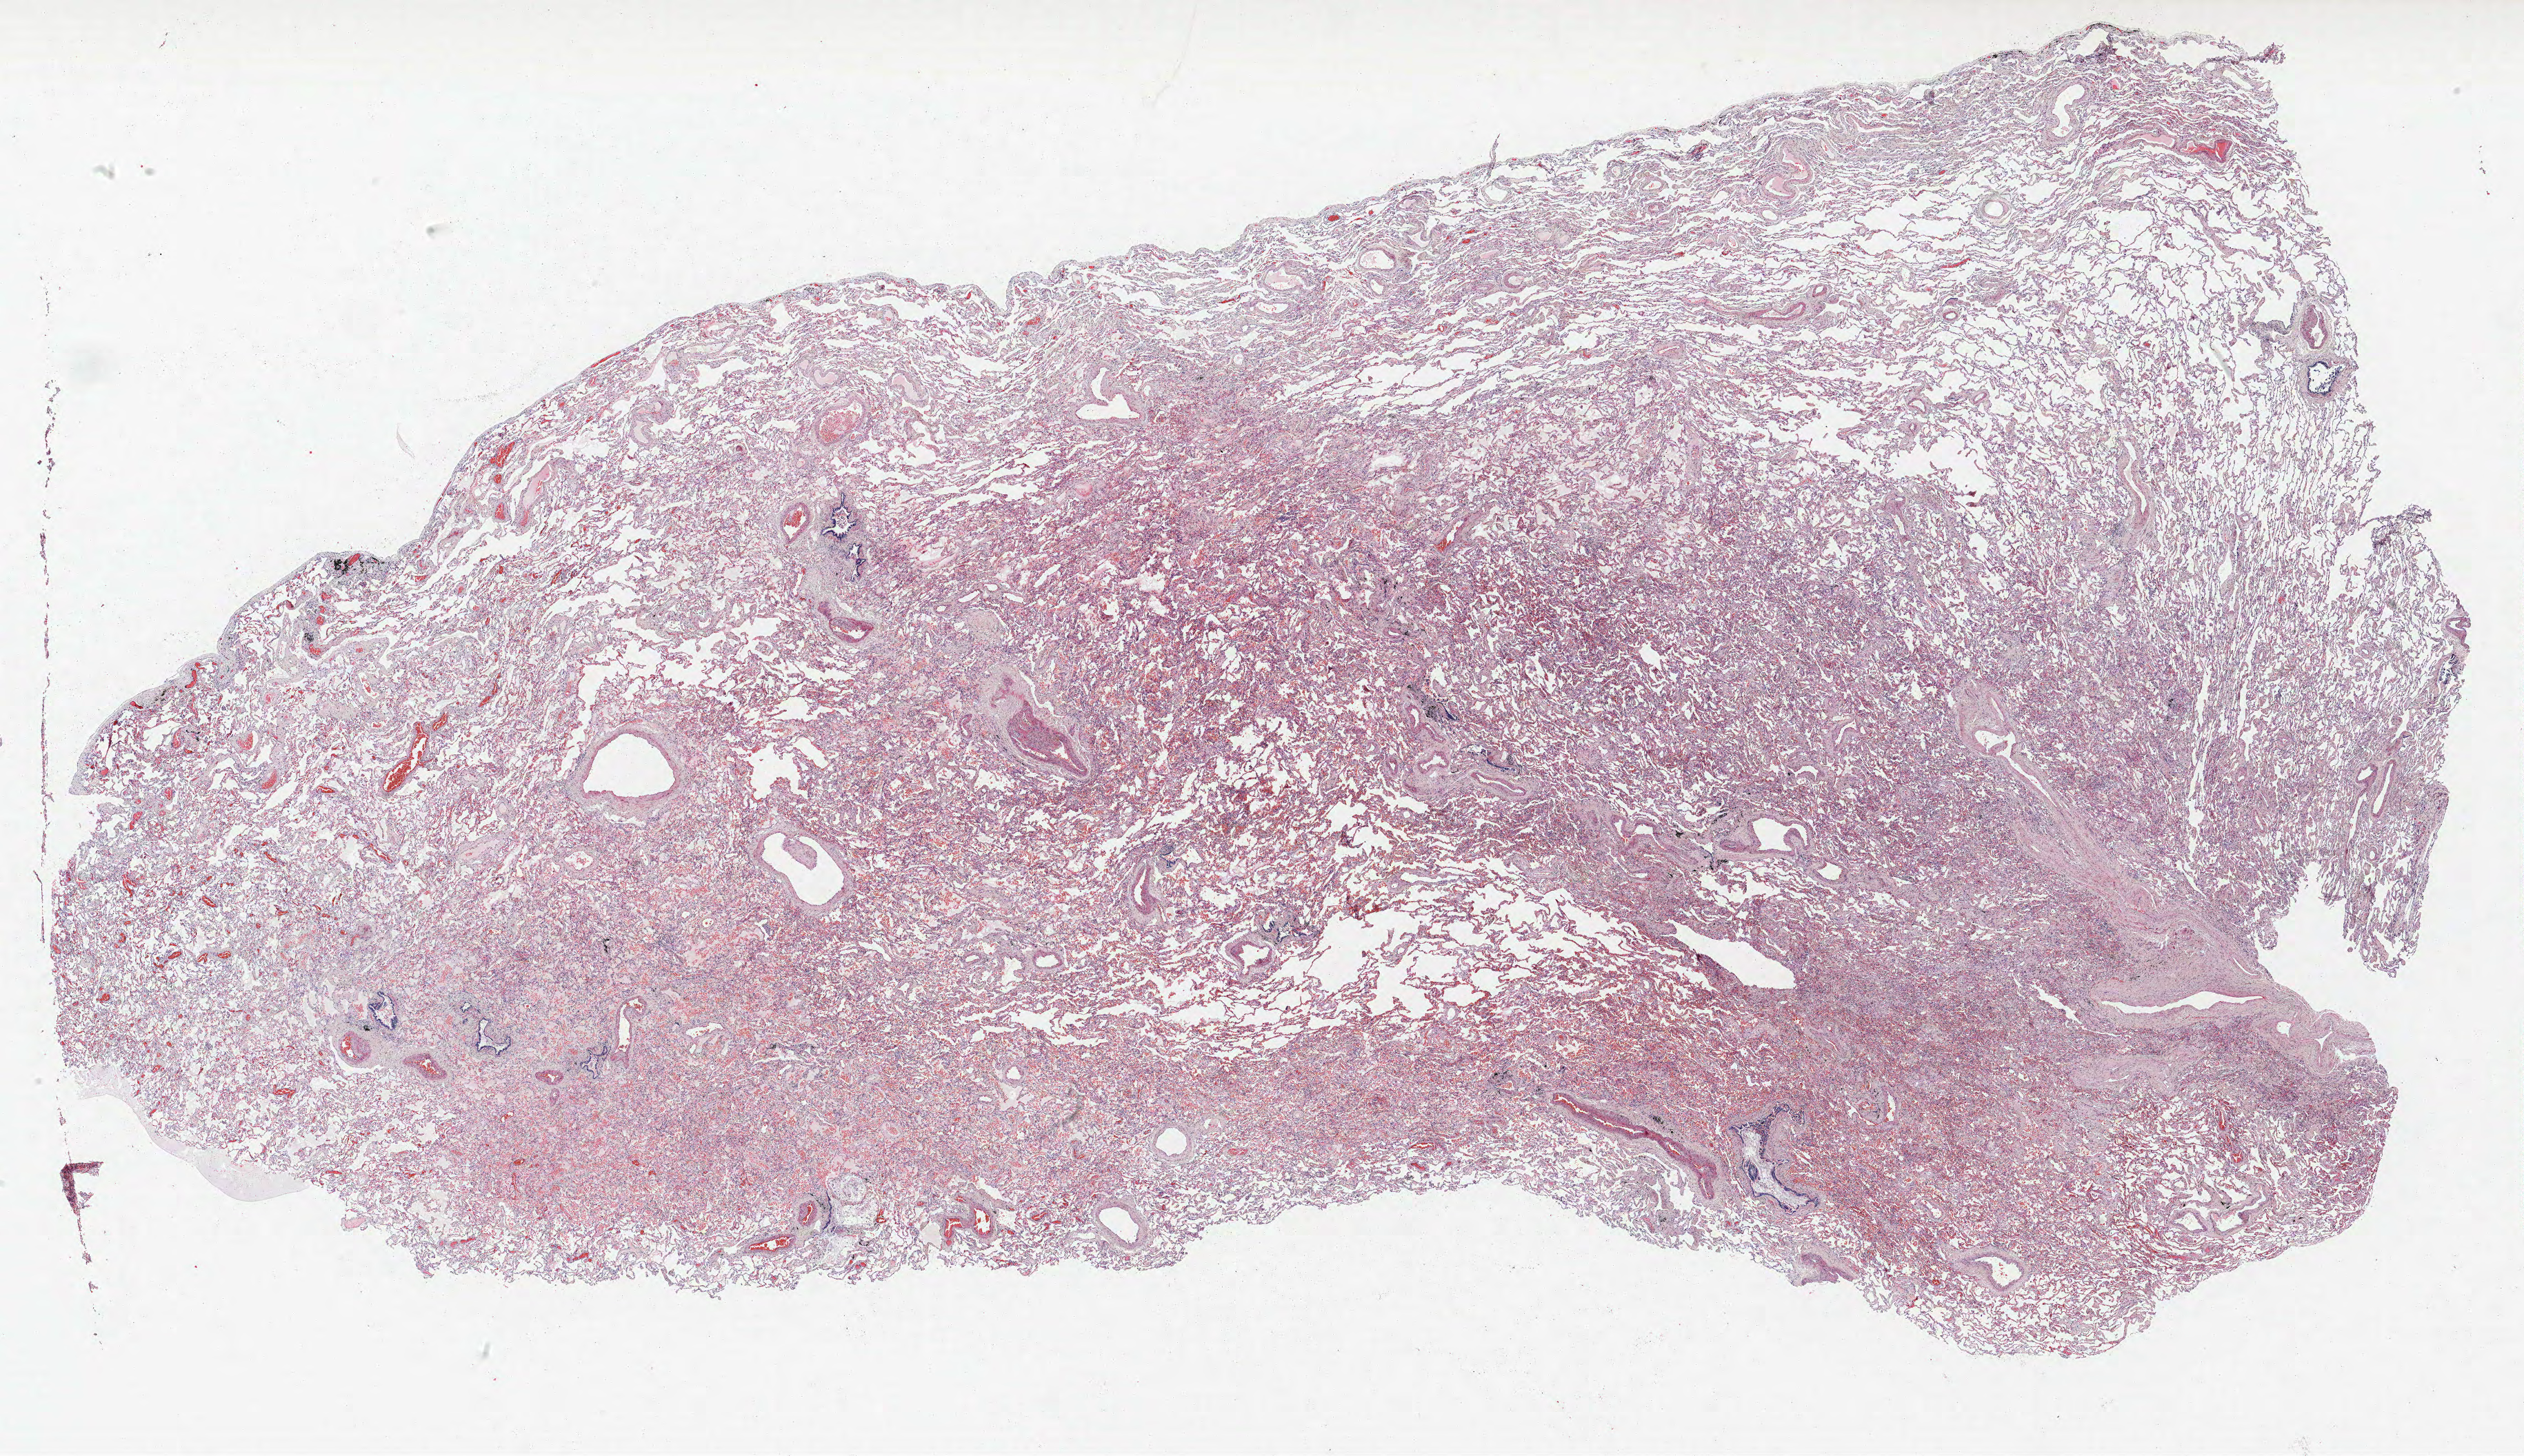
H&E whole-slide image — low-resolution overview of the scanned area, about 29.3 x 16.9 mm (acquisition: 40x scan), formalin-fixed paraffin-embedded (FFPE) section, lung. Female, age 68 at enrolment. Grade: poorly differentiated (G3).
* tumour size (pathology): 50 mm
* participant's lung-cancer diagnosis: Adenocarcinoma, NOS
* primary tumour location (clinical record): left upper lobe
* stage (AJCC 6th edition): IB